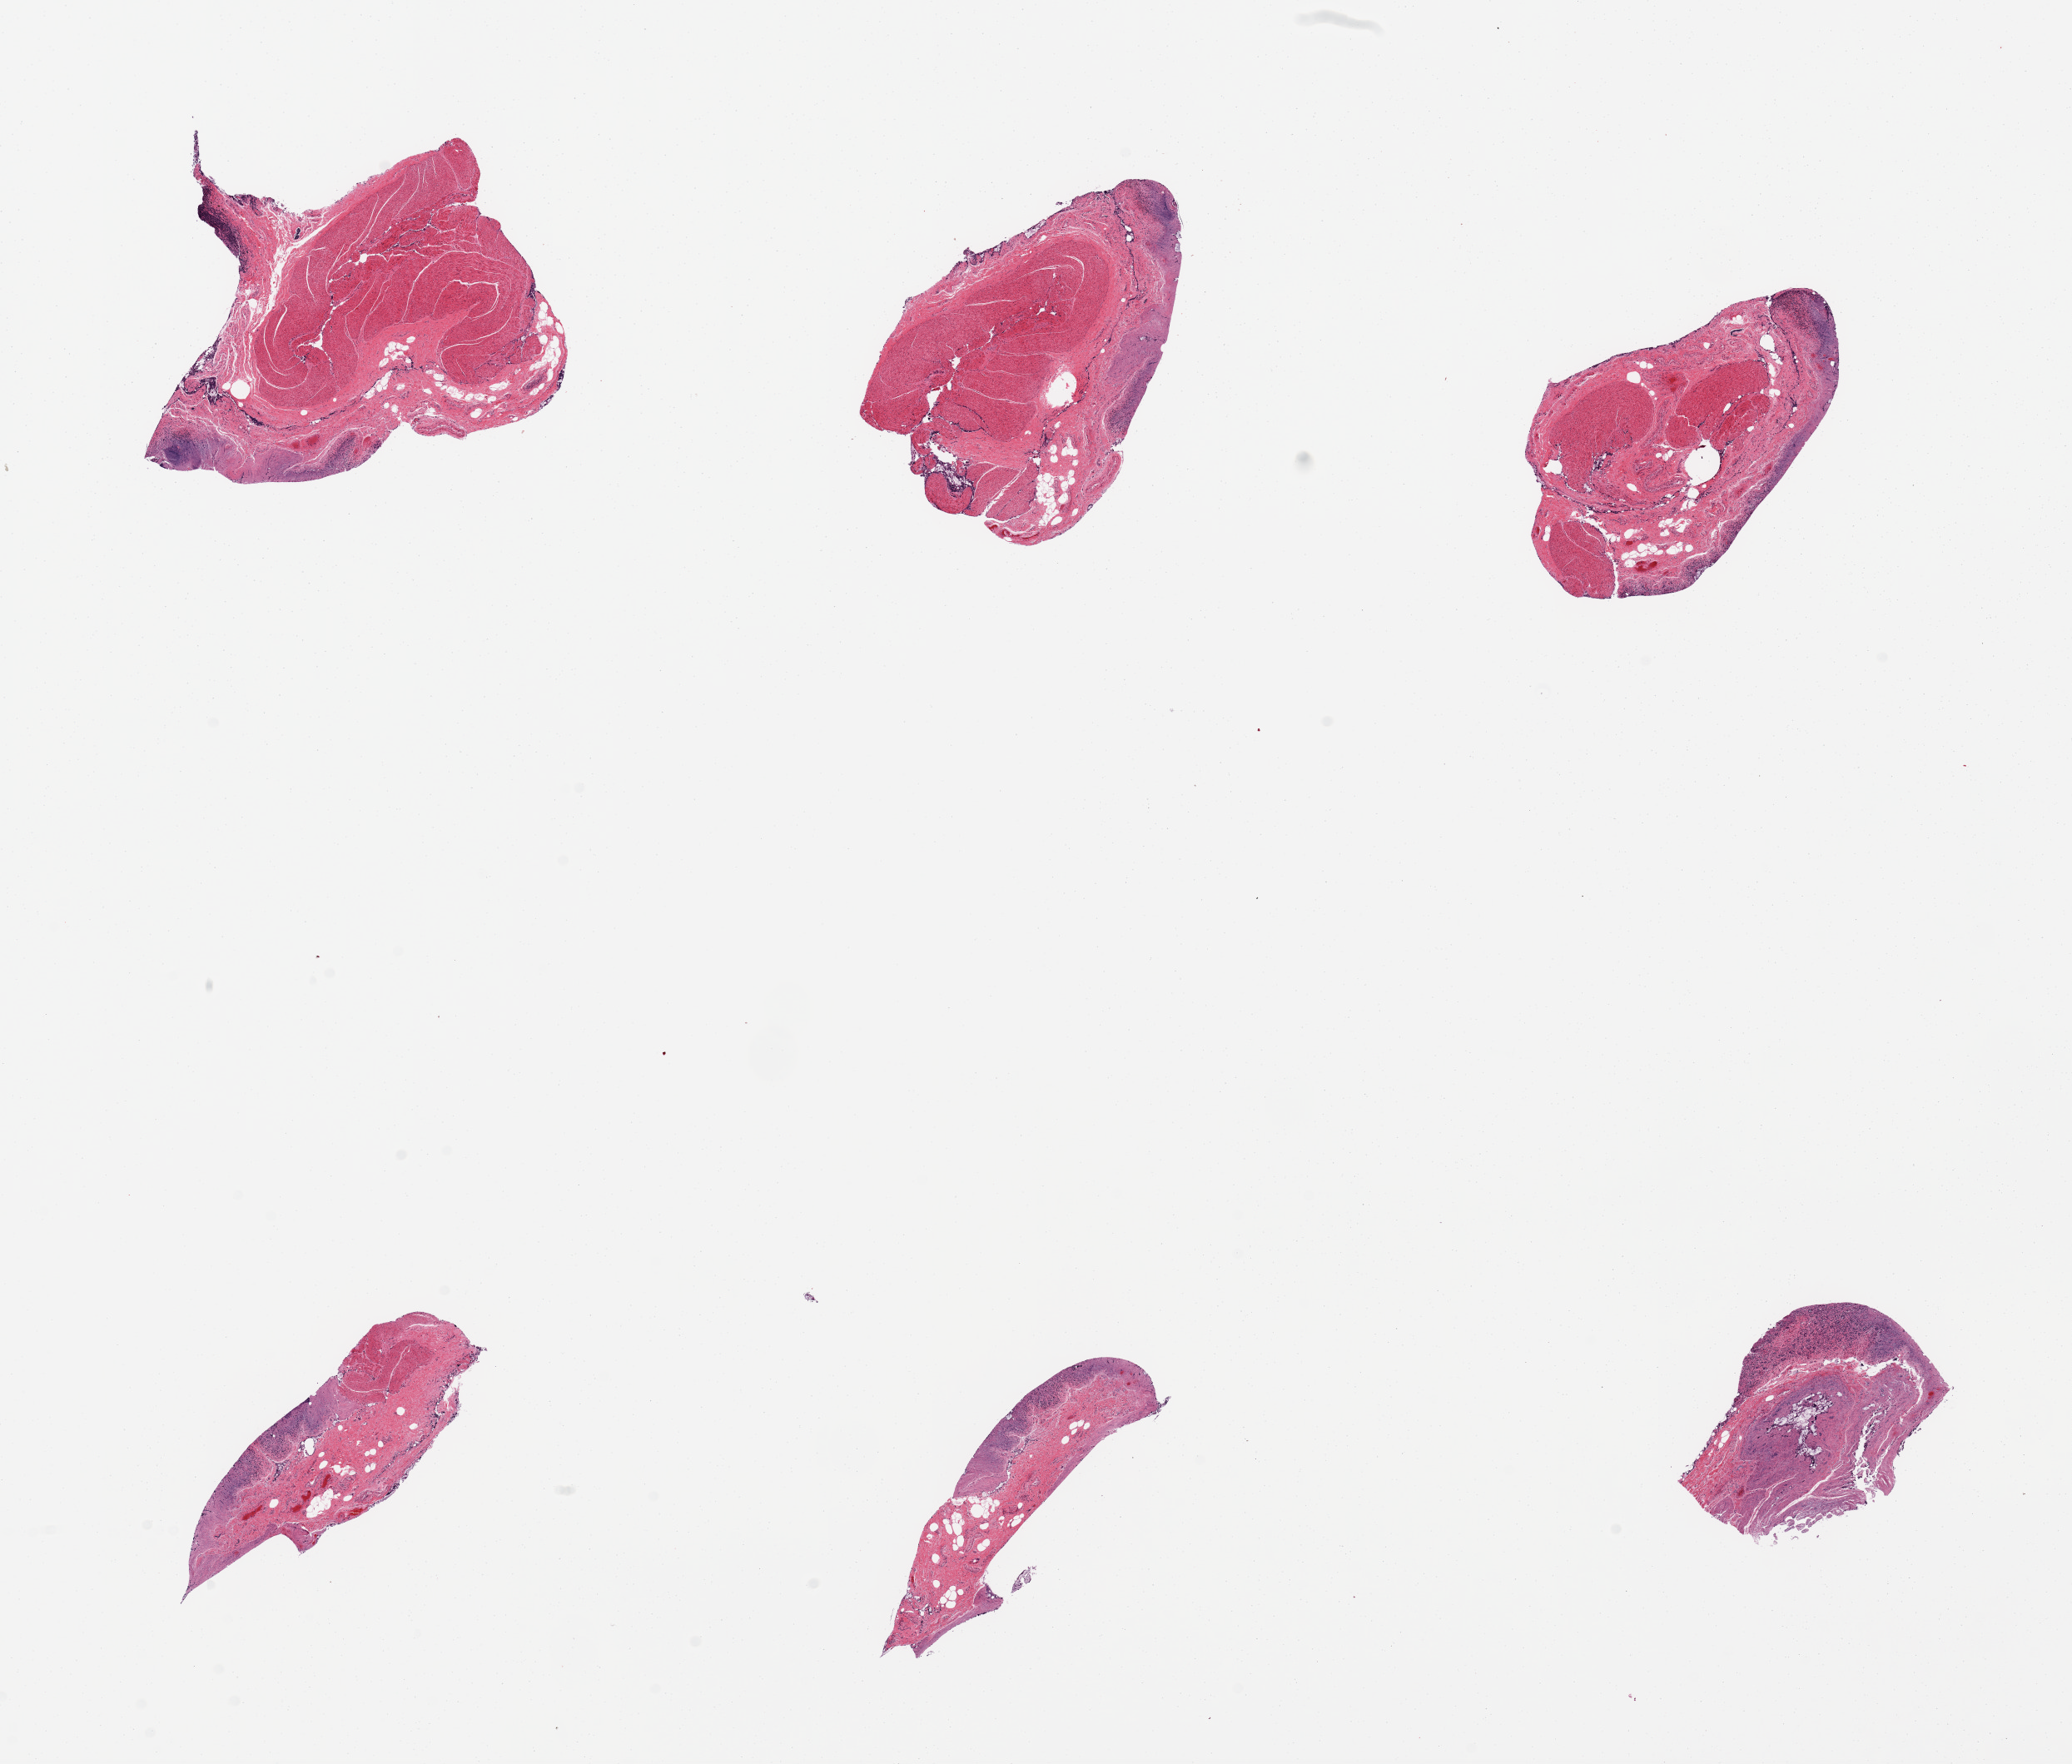
Whole-slide image, haematoxylin and eosin stain, brightfield, low-resolution overview of the scanned area, about 19.7 x 16.8 mm (acquisition: 20x scan); PAXgene-fixed paraffin-embedded (PFPE) section; sampled site (target tissue): ileum; donor tissue sample. Donor: male.
• pathologist's review note for this sample: 6 pieces, entirely autolyzed mucosa with limited lymphoid tissue and muscularis (not target)